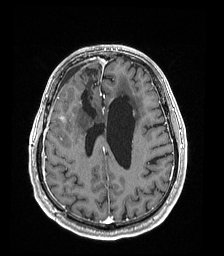
Brain MRI from a brain-tumour surgery series, one axial slice. Slice 65 of 192 in the series (ordered by position). T1-weighted post-contrast. 1 mm slice thickness. 224 × 256 image matrix, field of view 224 × 256 mm. Case-level facts recorded for this patient, not image findings: histopathology: Astrocytoma; WHO grade: 4; IDH mutation: yes.
Outlined on this slice (expert manual segmentation):
- previous resection cavity: bounding box <81,67,98,117> (left, top, right, bottom; pixels)